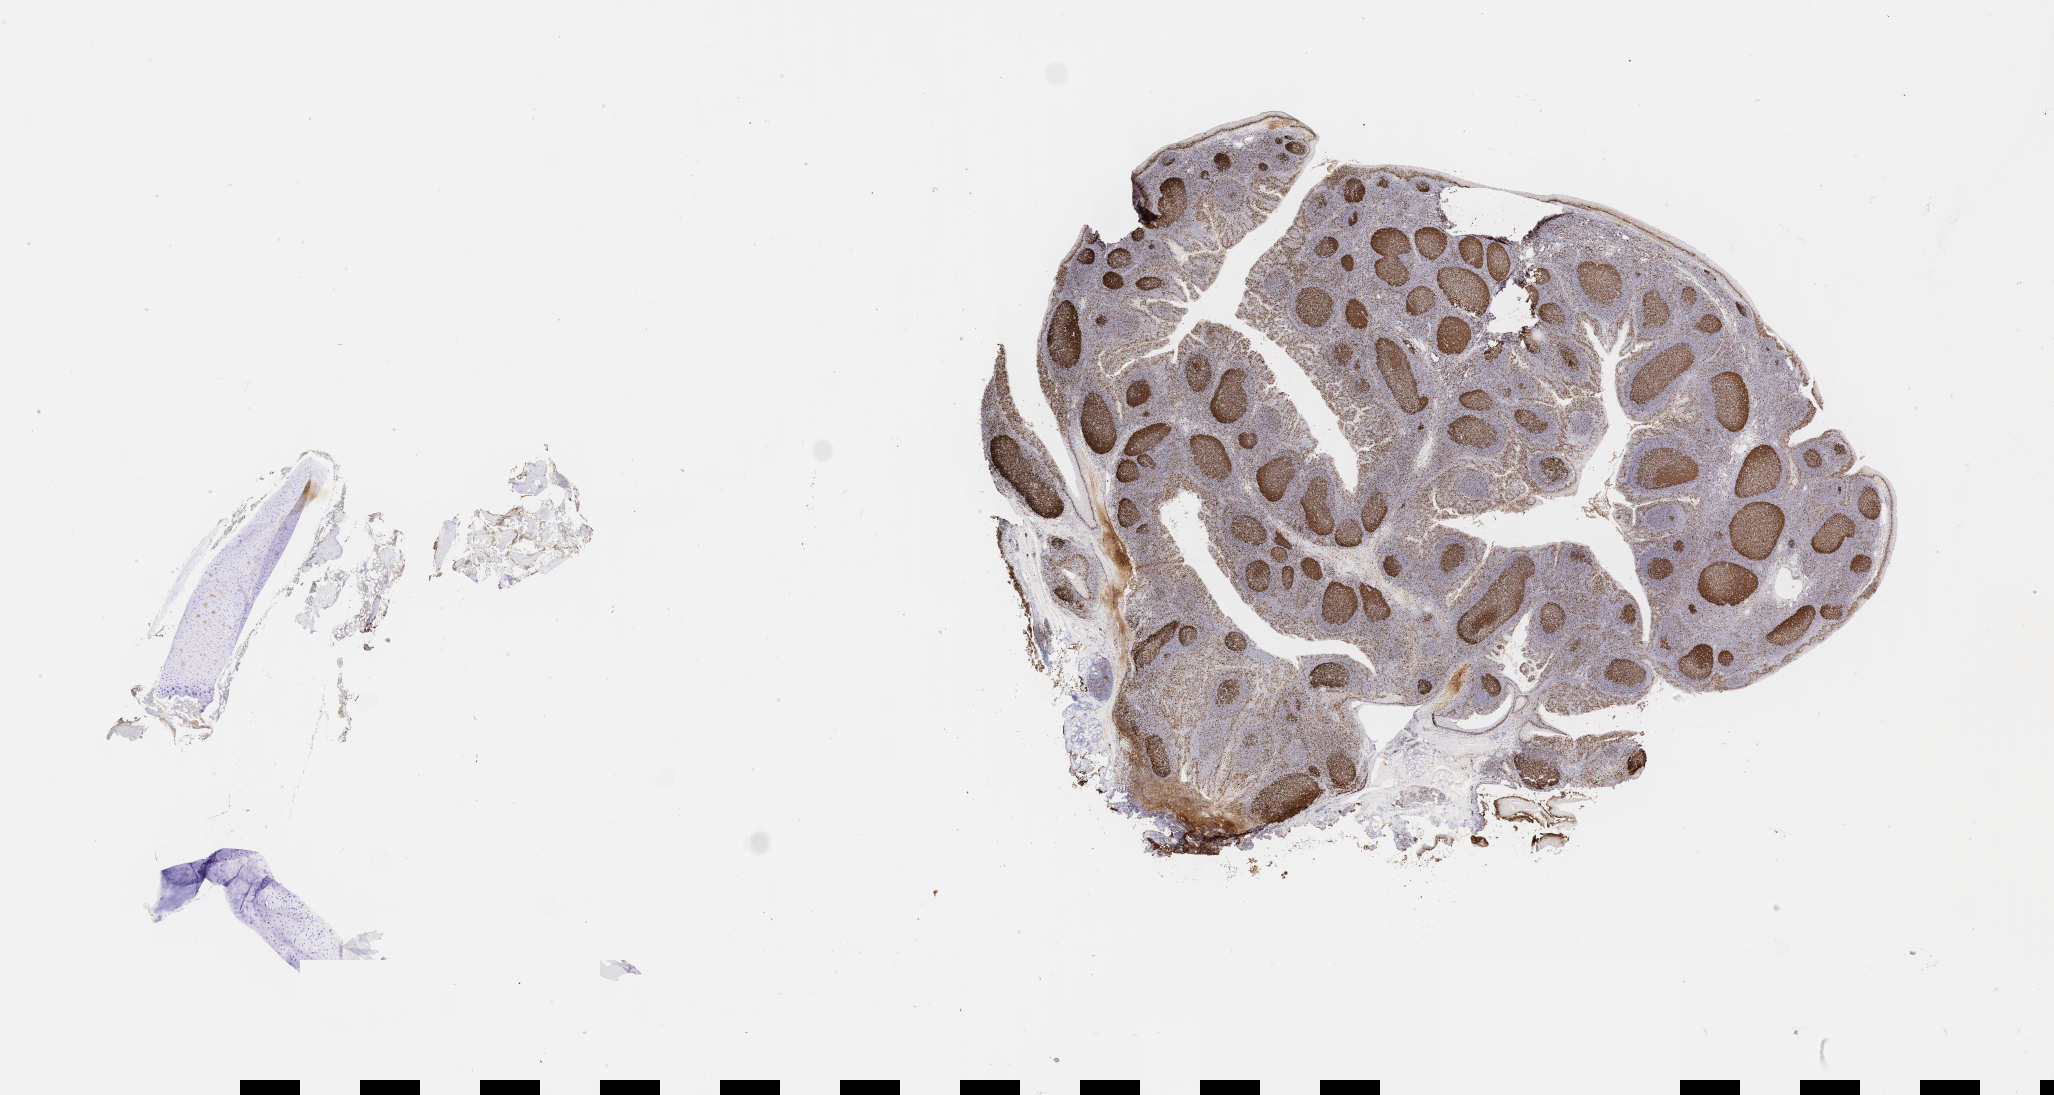
Immunohistochemistry (IHC) whole-slide image stained for Ki-67 — low-resolution overview of the scanned area, about 33.2 x 17.7 mm, tumor tissue, site: bone marrow. Patient female; age 11 years.
Diagnosis: Burkitt lymphoma, NOS.